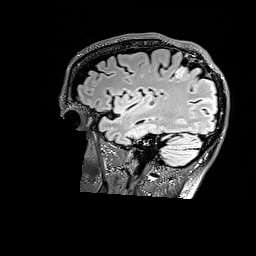
Brain MRI from a brain-tumour surgery series, one sagittal slice; position 126 of 176 along the scan axis; T2 FLAIR; 1 mm slice thickness; 256 × 256 image matrix, field of view 256 × 256 mm. Case-level facts recorded for this patient, not image findings: histopathology: Astrocytoma; WHO grade: 3; IDH mutation: yes.
Structures marked on this image (outlined manually by an expert reader):
- tumour: bounding box (x1, y1, x2, y2) in pixels: (176, 66, 188, 79)